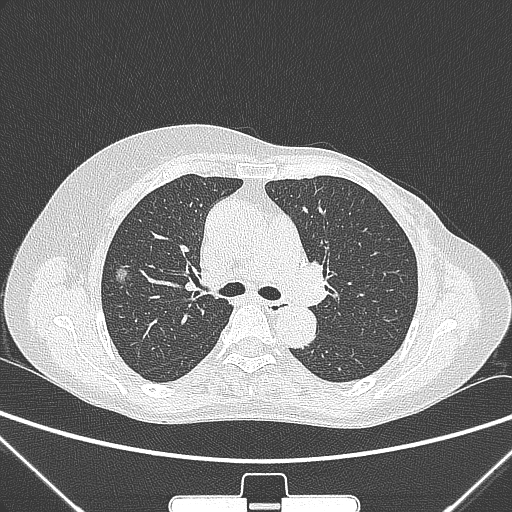
Chest CT, one axial slice. Slice 162 of 265 in the series (ordered by position). Lung window (W 1500 / L -600 HU). 1 mm slice thickness. 512 × 512 image matrix, field of view 350 × 350 mm. Patient: female, 64 years. Case-level facts recorded for this patient, not image findings: clinical TNM (as recorded): T1c N0 M0; histopathological grade: G1-2.
Outlined on this slice (bounding box drawn by a radiologist):
- lung tumour (recorded histology: adenocarcinoma): bounding box (x1, y1, x2, y2) in pixels: (109, 260, 131, 292)